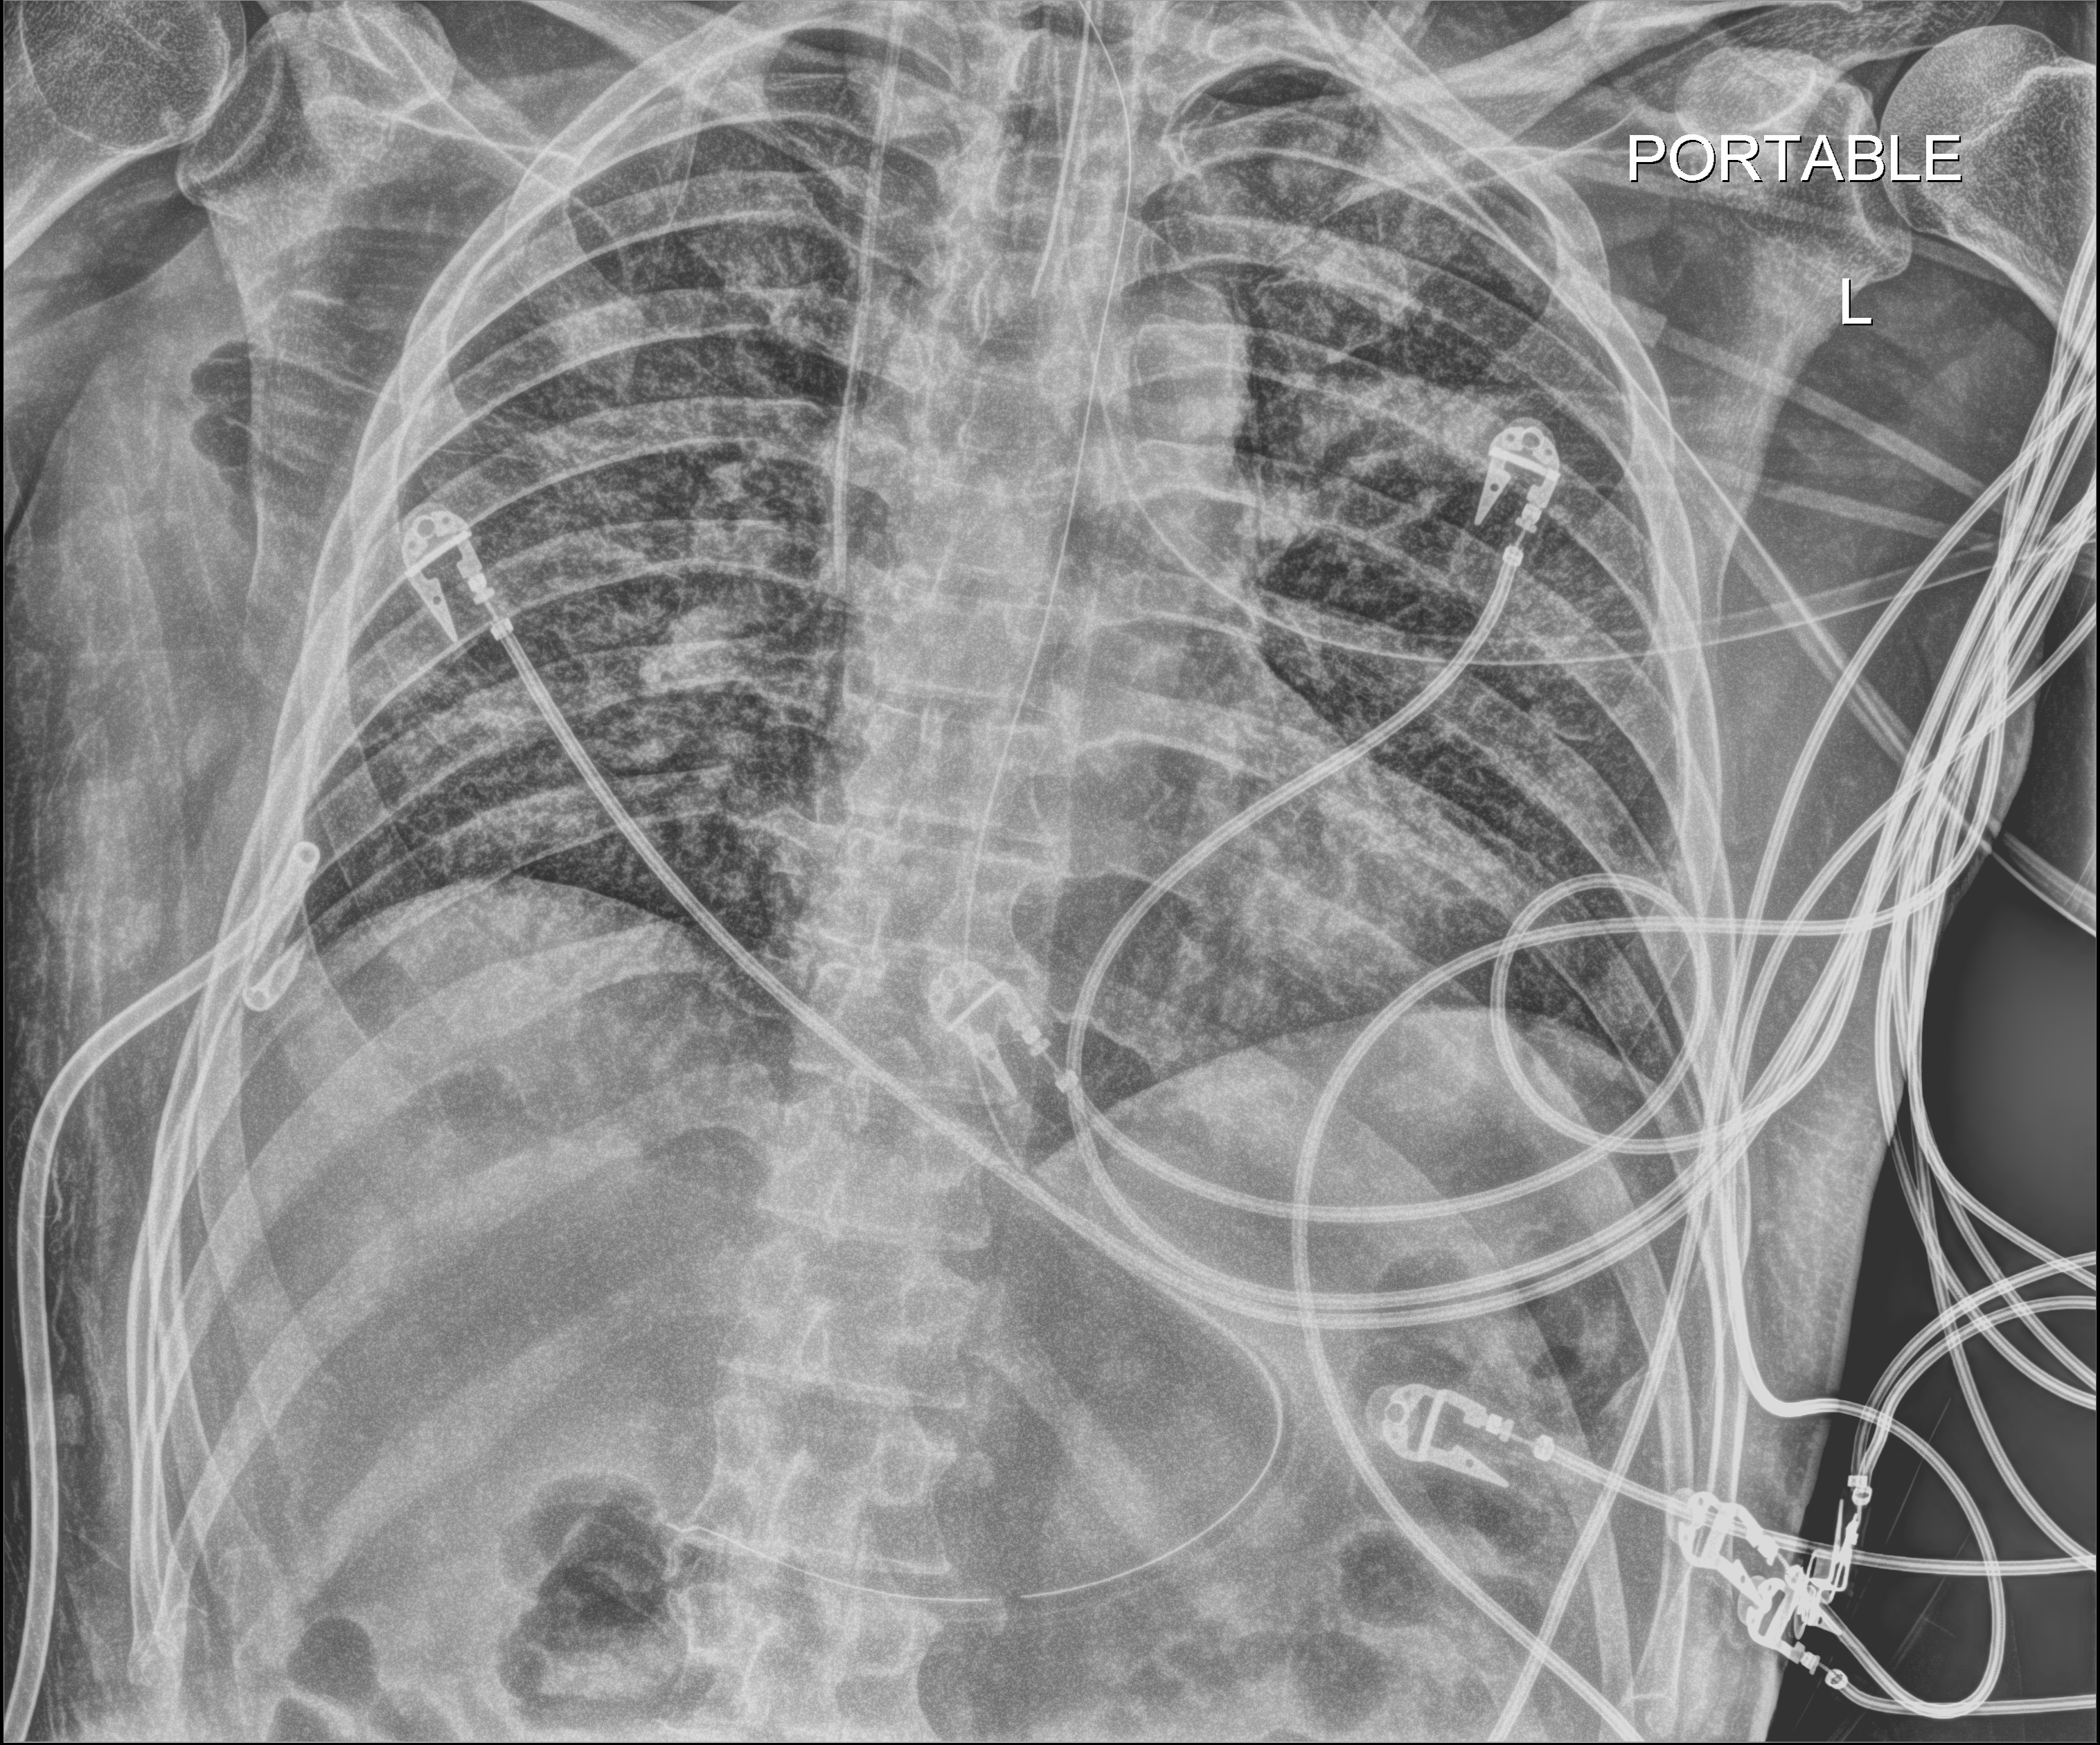
Portable chest radiograph; anteroposterior (AP) projection. Patient hospitalised with COVID-19; male, aged 18–59 years.
Hospital-stay facts (about this admission, not read from this image; timing relative to this image not recorded): diabetes (admission record): no.